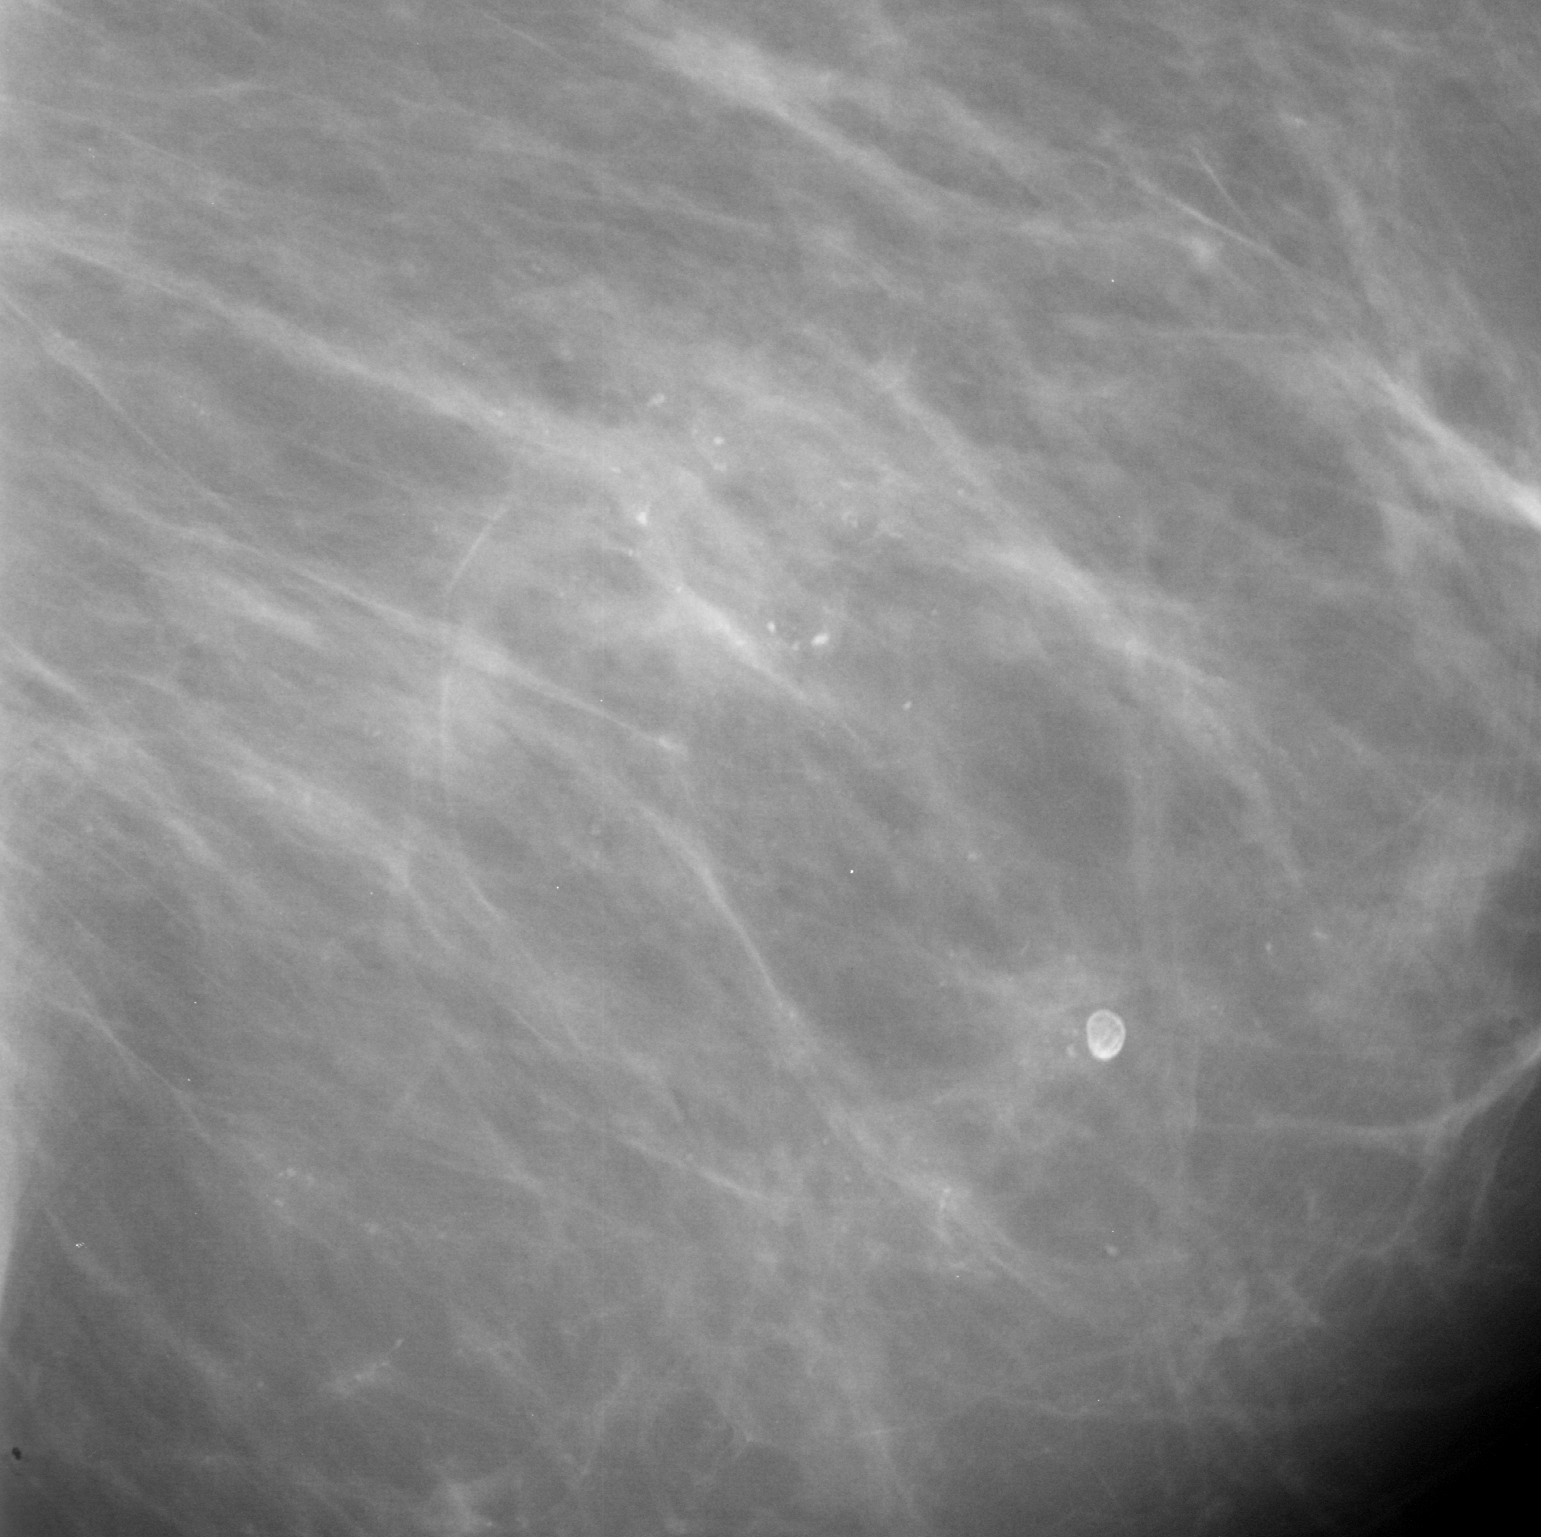
Cropped region of a digitized screen-film mammogram centred on a radiologist-marked abnormality, left breast, MLO view.
Finding: calcifications, morphology amorphous, distribution regional; BI-RADS assessment category 5; subtlety rating 3 on a 1 (subtle) to 5 (obvious) scale; pathology (as recorded): malignant.